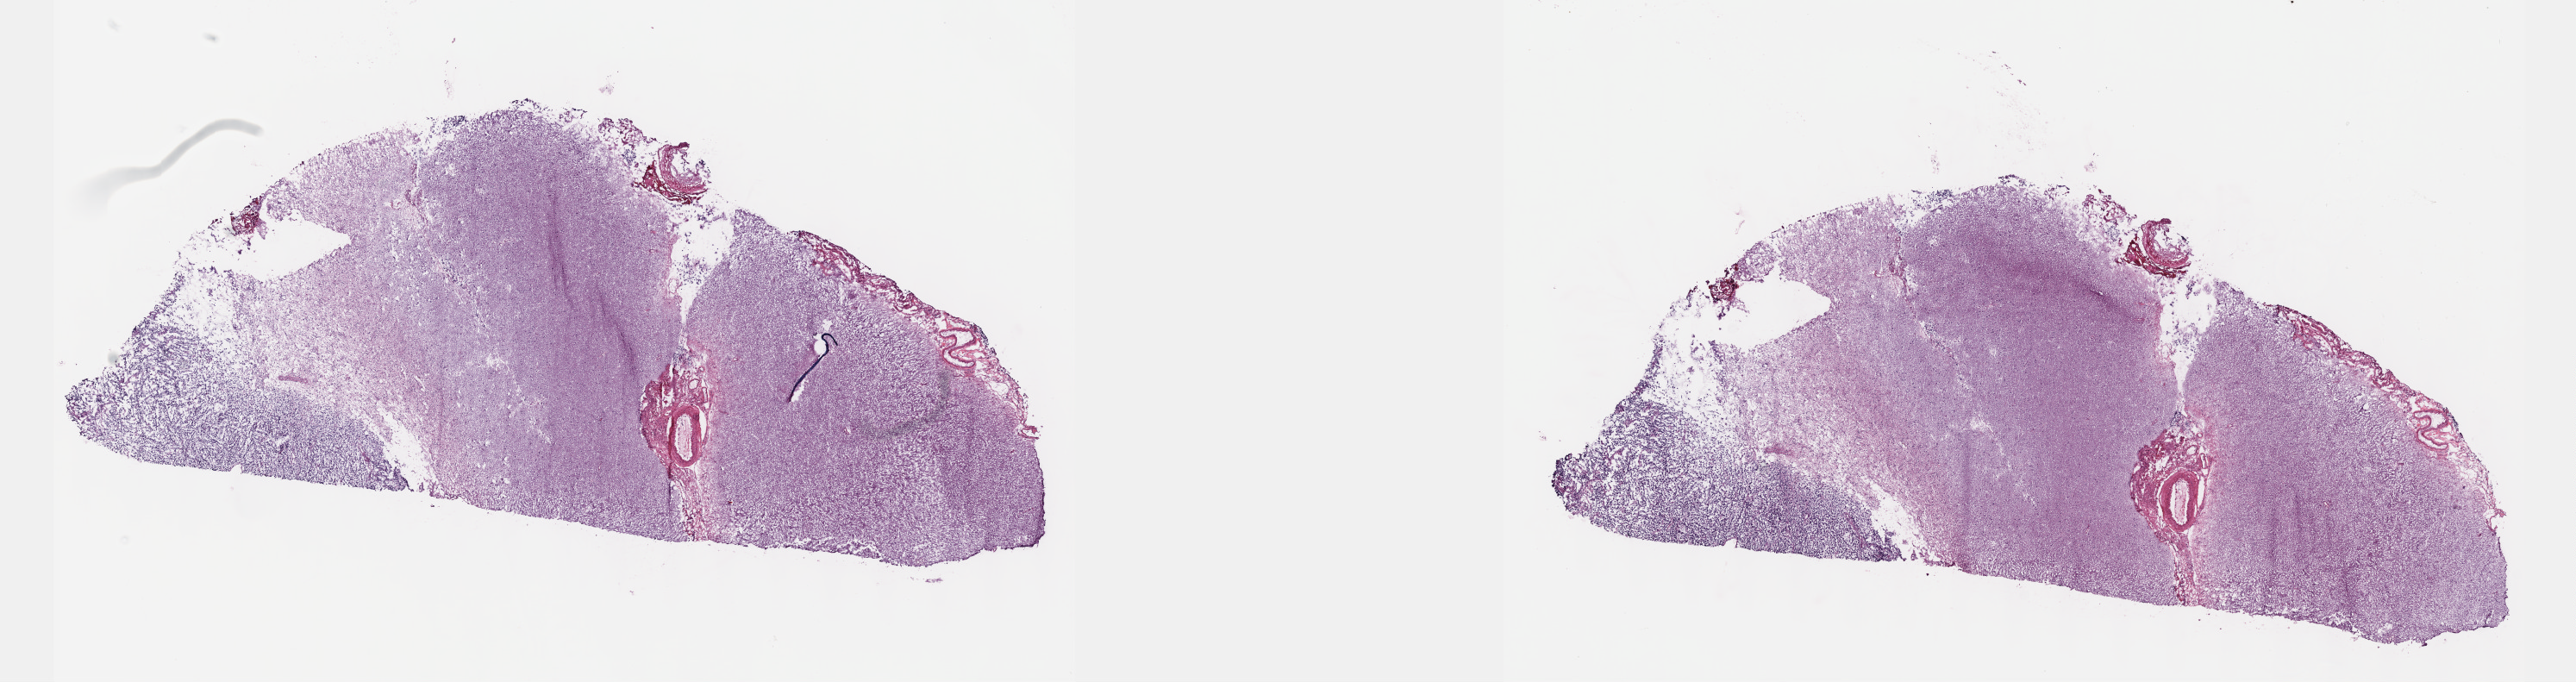
Whole-slide histology image, H&E — shown as a low-resolution overview of the whole scanned area (about 24.1 x 6.4 mm). Frozen section from the top of the tissue portion. Brain, primary tumour sample. Patient: female, age at initial diagnosis 73 years. Histologic grade: G3 (poorly differentiated). Composition of this section per pathologist review: tumour cells 30%, tumour nuclei 60%, normal cells 30%, stromal cells 40%, necrosis 0%. Inflammatory infiltration, as recorded: lymphocyte infiltration 0%, monocyte infiltration 0%, neutrophil infiltration 0%.
Histologic diagnosis: Oligodendroglioma, anaplastic (cerebrum). Laterality: right.